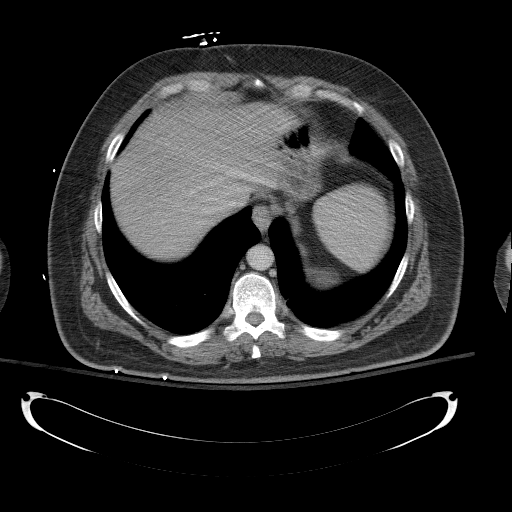
Contrast-enhanced abdominal CT, one axial slice. Position 101 of 154 along the scan axis. Reconstruction kernel B41f. 120 kVp. Intravenous contrast given. Soft-tissue window (W 400 / L 40 HU). 5 mm slice thickness. 512 × 512 image matrix, field of view 467 × 467 mm. Male patient, age 43 years. From the clinical record (not read from this slice): diagnosis: adrenocortical carcinoma; tumour side: left adrenal; tumour size at pathology: 9.8 cm; Ki-67 index: 30 %; stage (as recorded): 2.
Structures marked on this image (semi-automatic segmentation, software-assisted and operator-edited):
- mass: bounding box <314,272,328,282> (left, top, right, bottom; pixels)